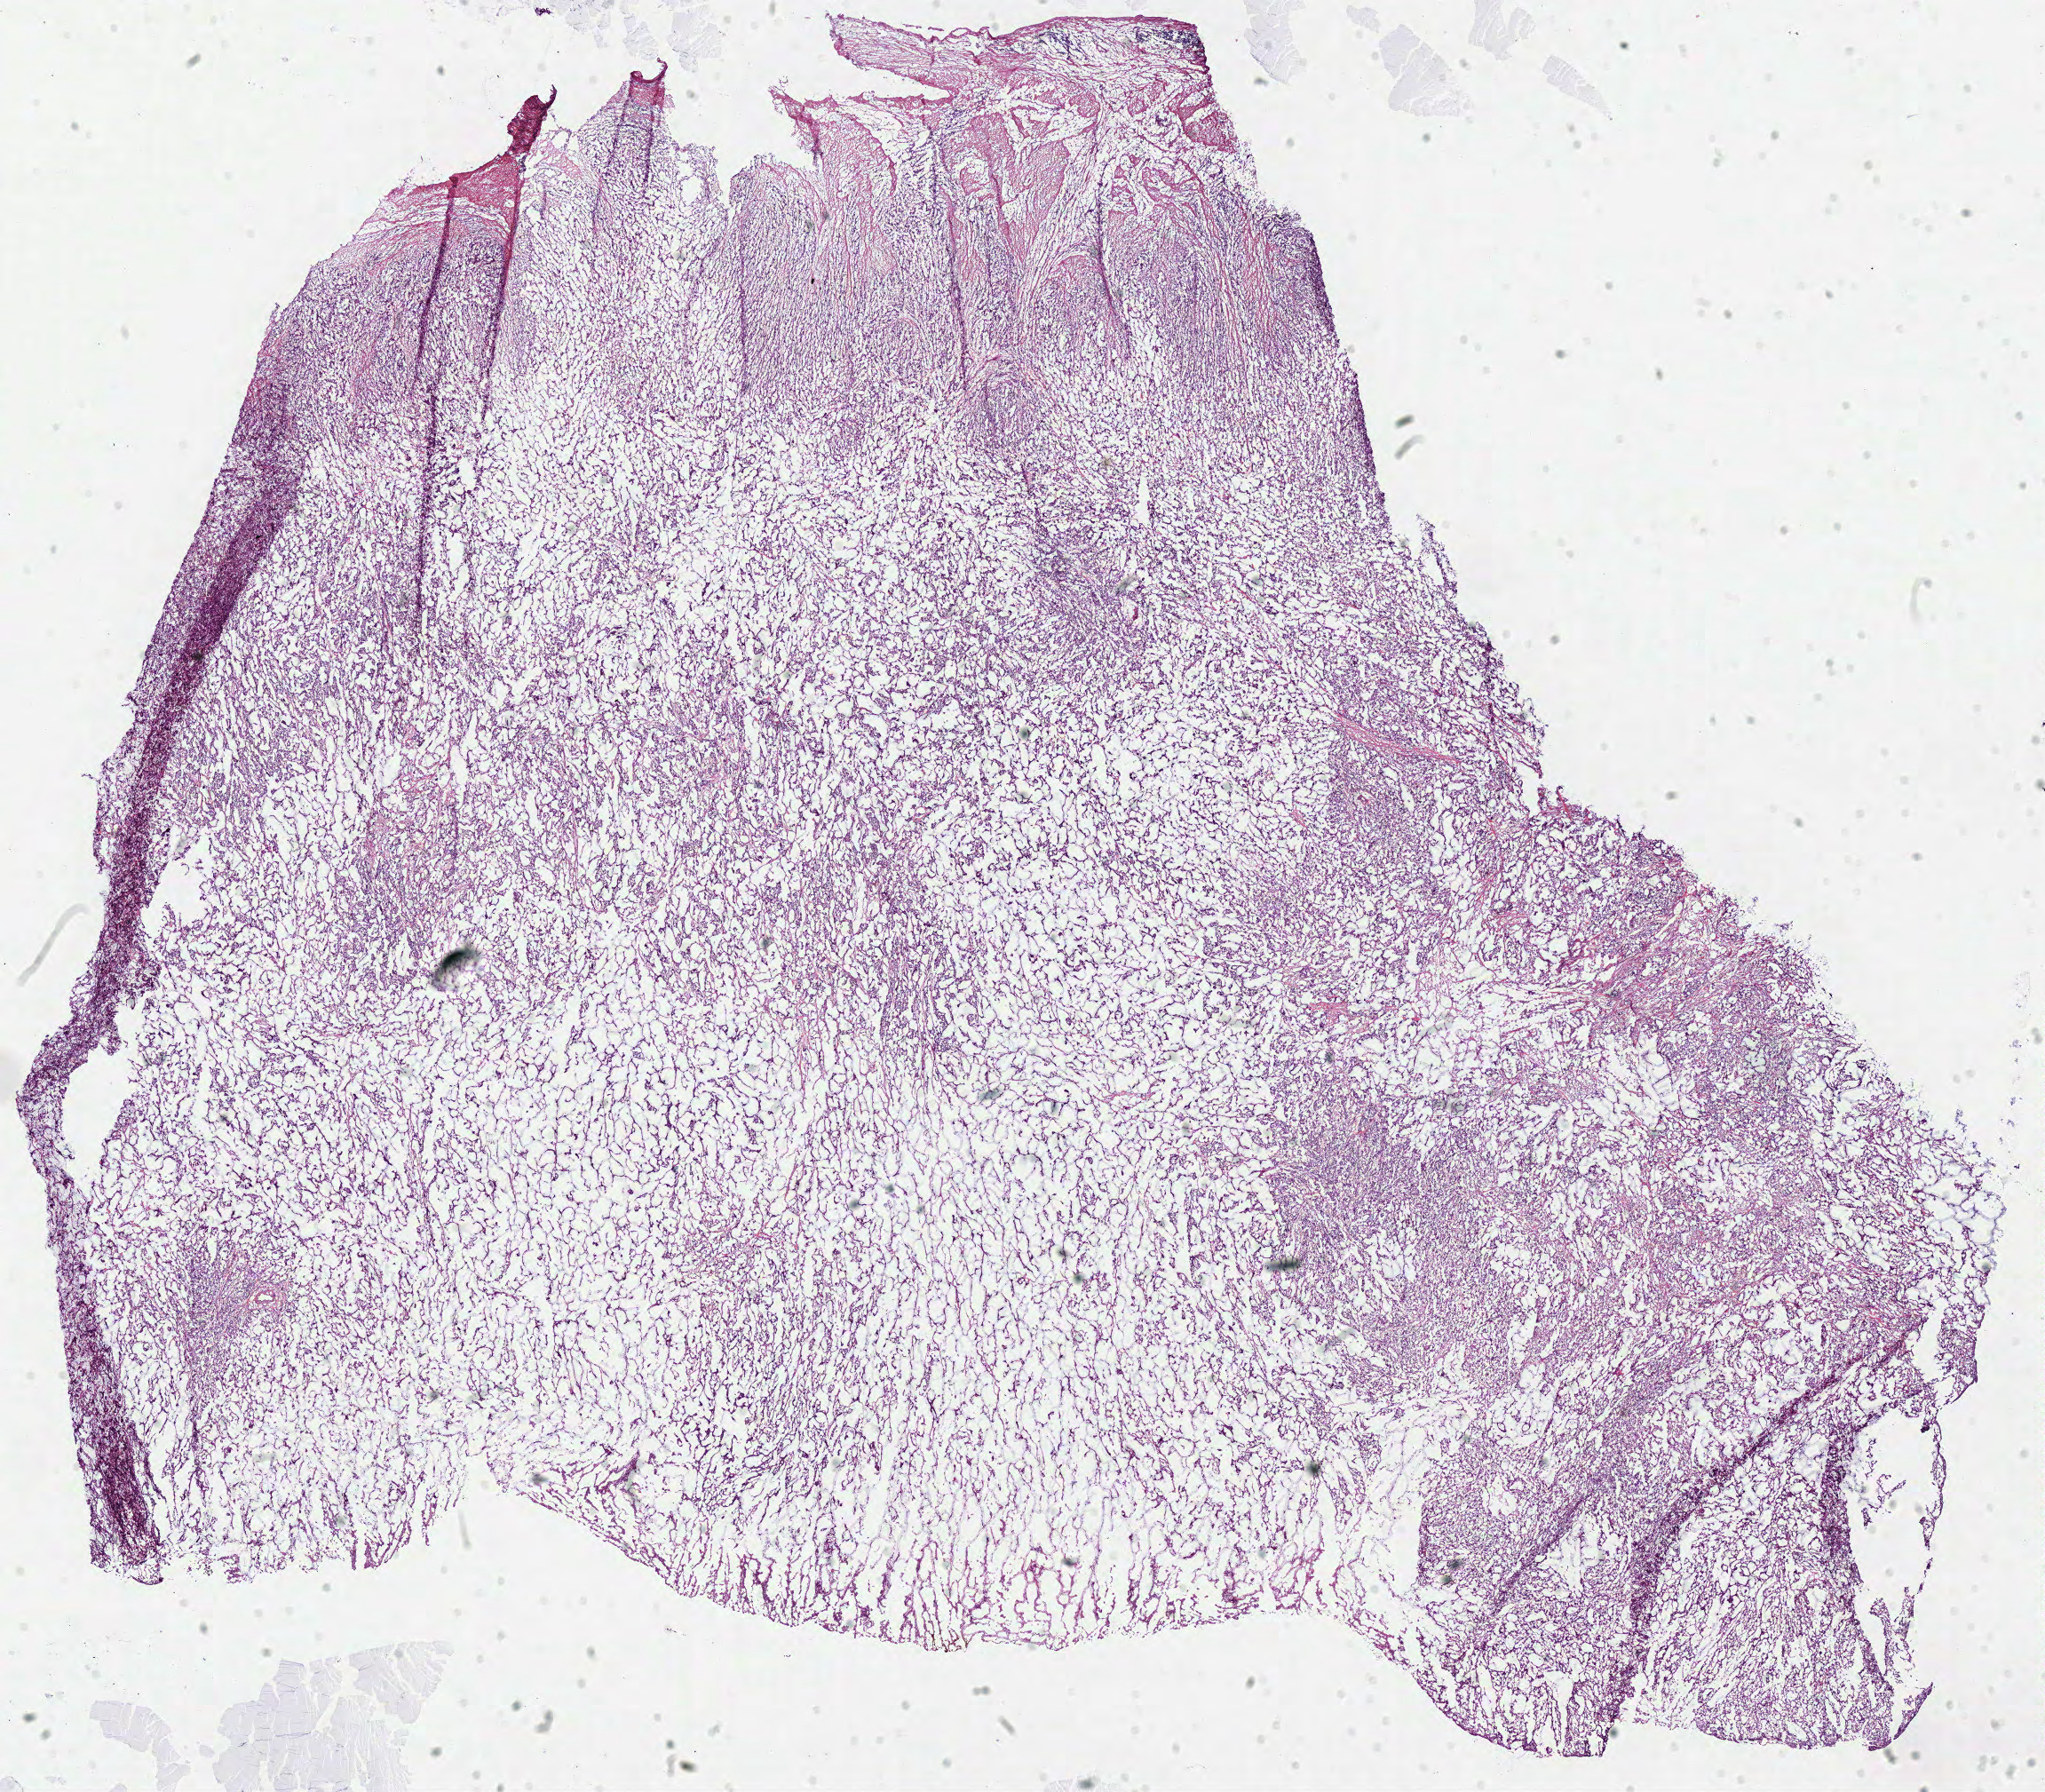
Whole-slide histology image, H&E-stained, low-resolution overview of the scanned area, about 18.1 x 15.9 mm (from a 40x scan); frozen section from the top of the tissue portion; primary tumour sample from the stomach. Female, age 64 years at initial diagnosis. Histologic grade: G3 (poorly differentiated). Slide review estimates, as recorded: tumour cells 80%, tumour nuclei 80%, normal cells 0%, stromal cells 20%, necrosis 0%.
Histologic diagnosis: Adenocarcinoma, NOS (body of stomach). AJCC pathologic stage: IIA (7th edition). Lymph nodes positive (case pathology): 0 of 3 examined.